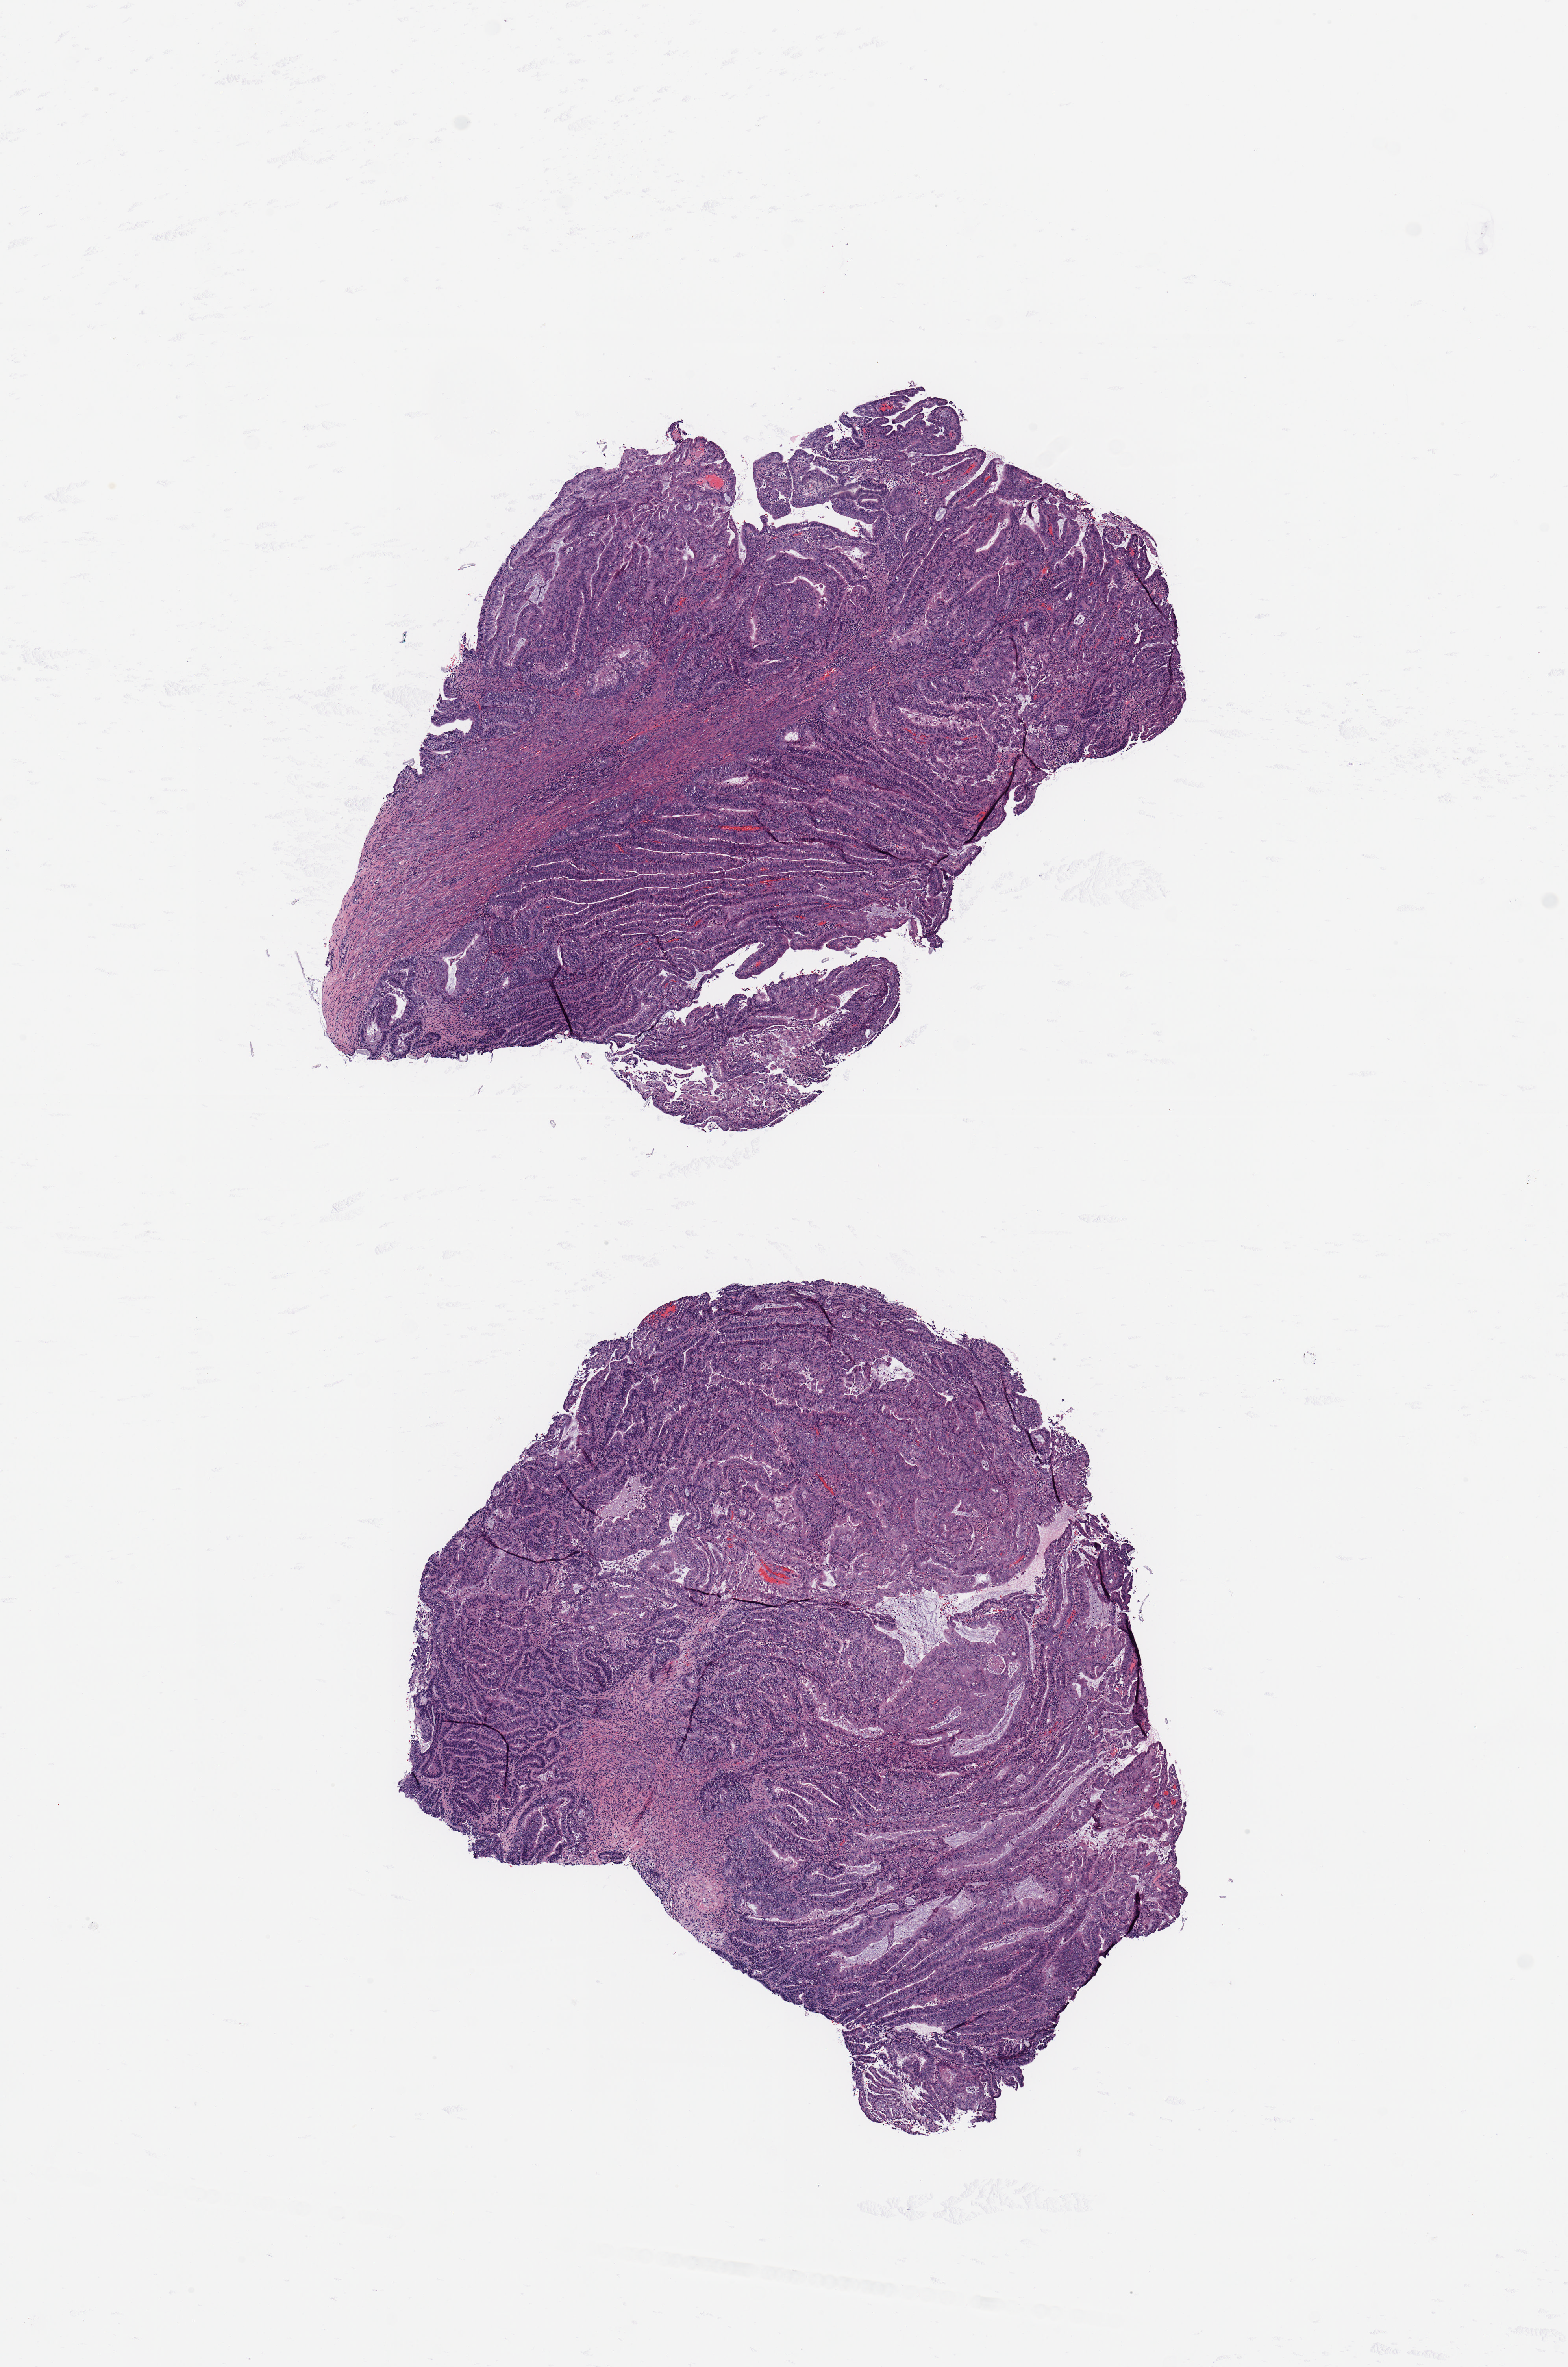
Digitized H&E-stained tissue section (whole slide), a low-resolution overview of the entire scanned area, about 7.9 x 11.9 mm (acquisition: 20x scan). Tumour tissue sample, uterus. Female, 64 y/o. Histologic grade: G2 (moderately differentiated).
Primary tumour site (as recorded): anterior endometrium. AJCC pathologic stage: III. Diagnosis: Endometrioid adenocarcinoma, NOS.